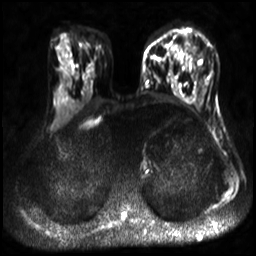
Breast MRI, one axial slice; position 13 of 30 along the scan axis; diffusion-weighted series; image 2 of 4 stored at this slice position (different b-values; order by instance number); 3 T; 4 mm slice thickness; 256 × 256 image matrix, field of view 320 × 320 mm. Female patient.
Structures marked on this image (outlined manually by an expert reader):
- tumour on diffusion-weighted imaging: box from (x=184, y=38) to (x=199, y=55) px